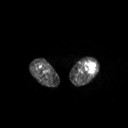
FDG PET of an extremity soft-tissue mass (from a PET/CT study), one axial slice. Slice 199 of 267 in the series (ordered by position). 3.27 mm slice thickness. 128 × 128 image matrix, field of view 700 × 700 mm. Female patient, age 62 years. From the clinical record (not read from this slice): histological type: undifferentiated – high grade; grade: high; site of the primary tumour: left thigh.
Structures marked on this image (expert contour drawn on MRI and transferred to this co-registered scan by the dataset authors):
- gross tumour volume including surrounding oedema: bounding box [x1, y1, x2, y2] px = [84, 62, 96, 73]